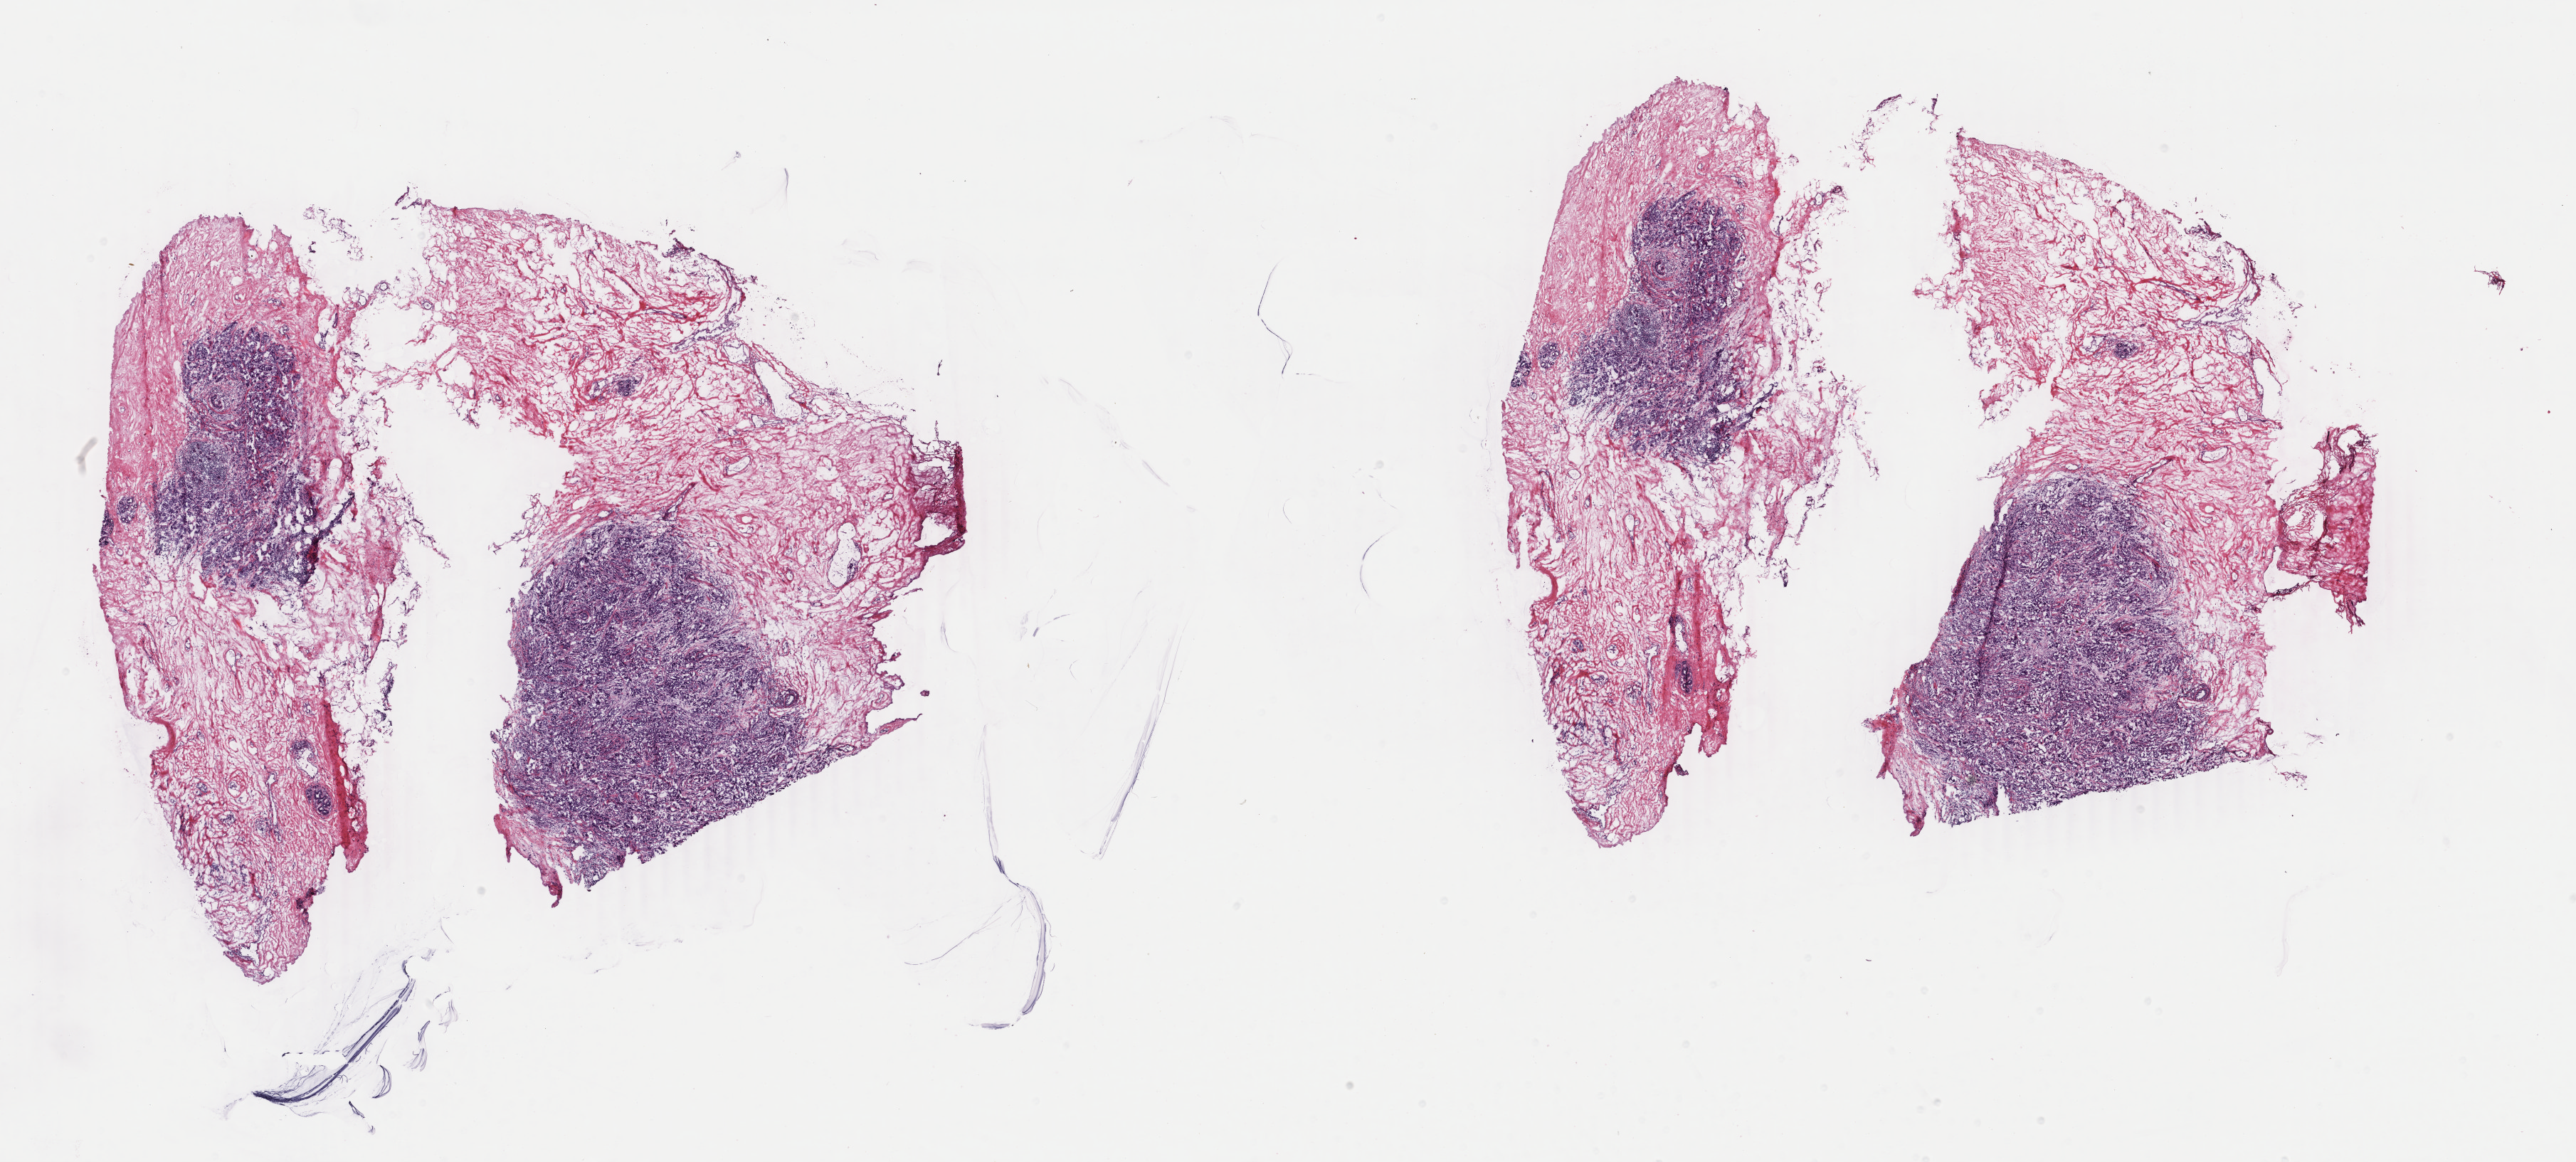
H&E-stained whole-slide image, shown as a low-resolution overview of the whole scanned area (about 28.8 x 13.0 mm, from a 40x scan); frozen section; primary tumour sample from the breast. Female patient; age at initial diagnosis 59 years. Composition of this section per pathologist review: tumour cells 75%, tumour nuclei 75%.
Histologic diagnosis: Infiltrating duct carcinoma, NOS.